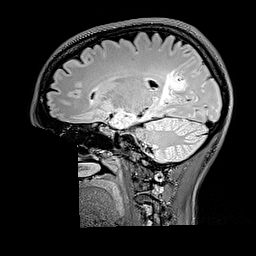
Brain MRI from a brain-tumour surgery series, one sagittal slice; position 104 of 176 along the scan axis; T2 FLAIR; 256 × 256 image matrix, field of view 256 × 256 mm. Case-level facts recorded for this patient, not image findings: histopathology: Oligodendroglioma; WHO grade: 2.
Outlined on this slice (manually delineated by an expert):
- tumour: box from (x=160, y=69) to (x=186, y=105) px